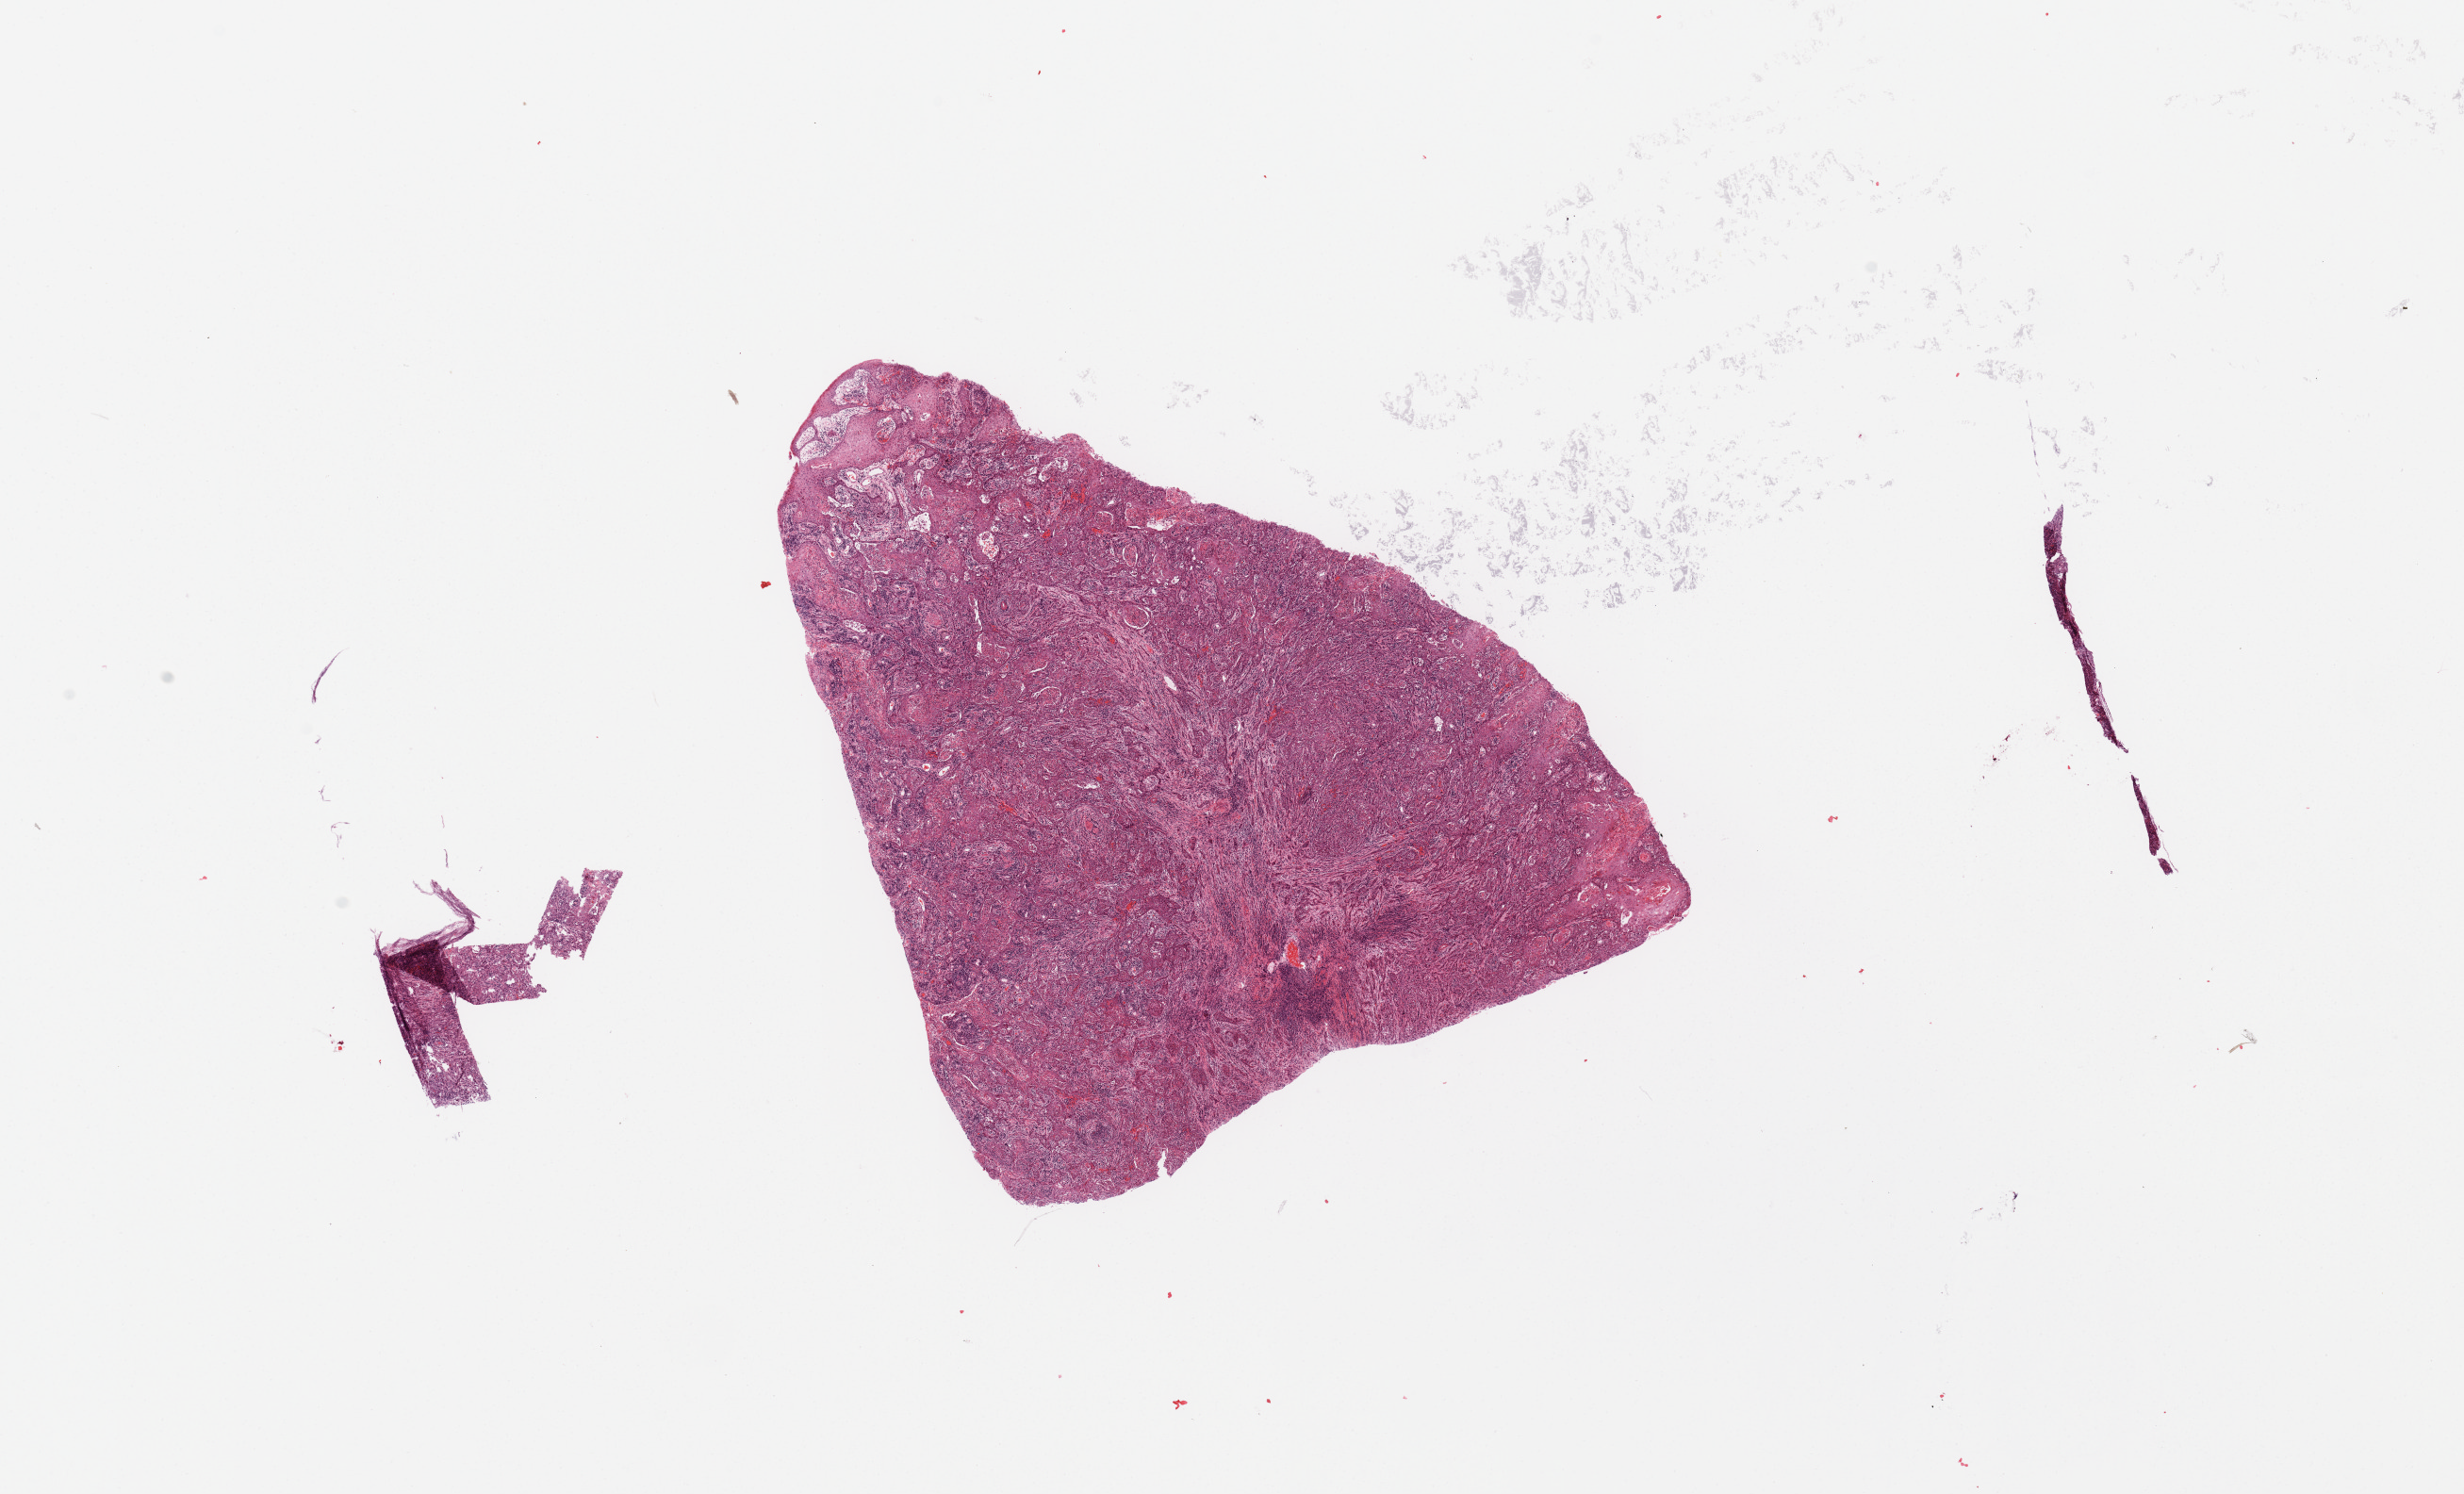
Whole-slide histology image, Hematoxylin and eosin (H&E) stained, shown as a low-resolution overview of the whole scanned area (about 20.7 x 12.5 mm). Tumour tissue sample, sampled site: tongue. Female, 68 y/o. Histologic grade: G2 (moderately differentiated). Pathologist review of this section (percent, as recorded): tumour nuclei 80%, necrosis 2%.
- primary tumour site (as recorded): oral cavity
- AJCC pathologic stage: IV
- diagnosis: Squamous cell carcinoma, NOS